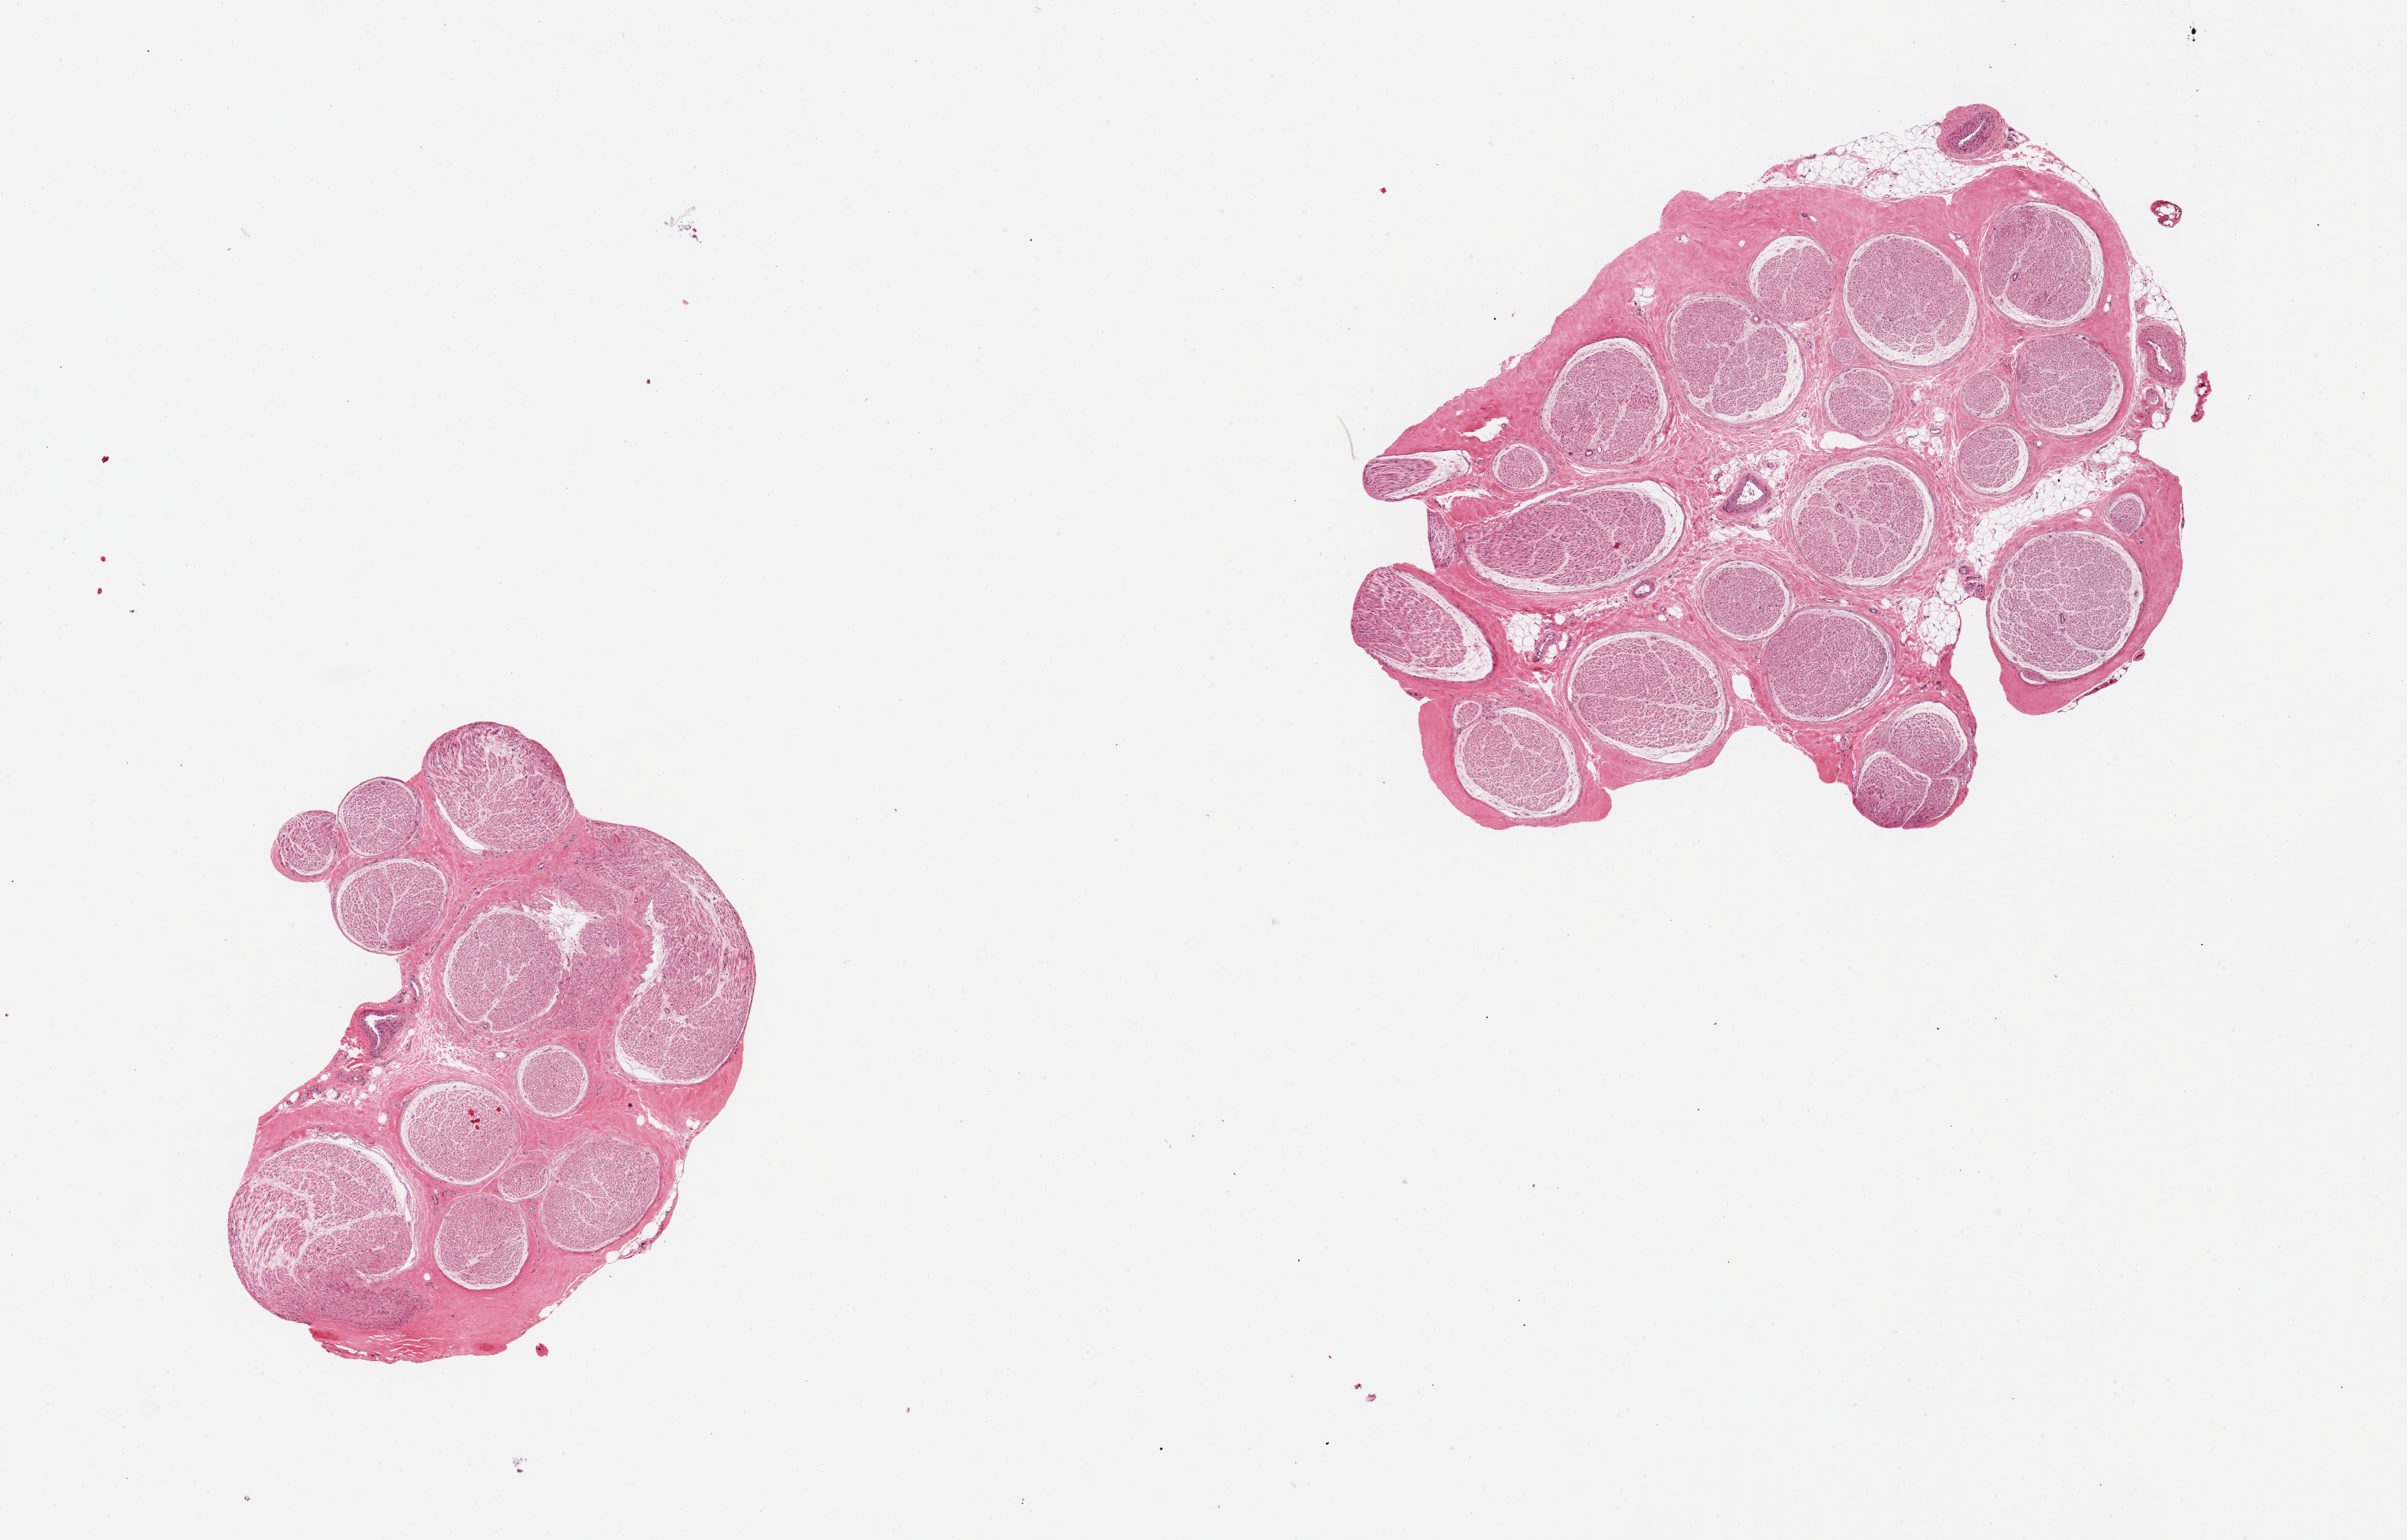
Whole-slide image, haematoxylin and eosin stain — low-resolution overview of the scanned area, about 13.8 x 8.8 mm (slide scanned at 20x). PAXgene-fixed, paraffin-embedded tissue. Section of tibial nerve (target tissue). Tissue donor sample.
Review note (as recorded): 2 pieces, ~5% fat (internal and attached) on one piece.